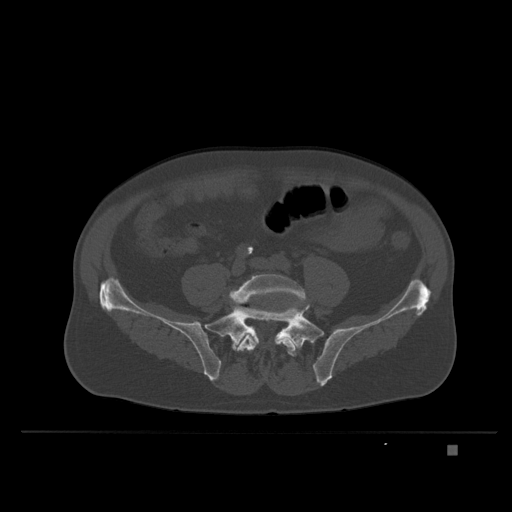
CT including the spine, one axial slice; position 48 of 435 along the scan axis; bone window (W 1800 / L 400 HU); 1.5 mm slice thickness; 512 × 512 image matrix, field of view 434 × 434 mm. Patient: male, 73 years. From the clinical record (not read from this slice): primary cancer: skin.
Outlined on this slice (semi-automatically segmented with operator editing):
- L5 vertebra: bounding box [x1, y1, x2, y2] px = [229, 274, 306, 364]